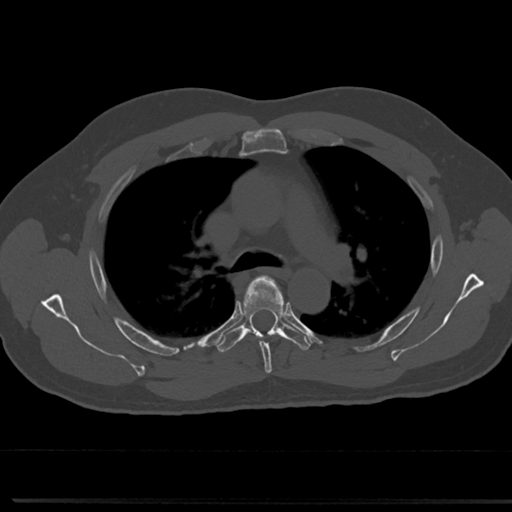
CT including the spine, one axial slice. Reconstruction kernel Br40s/3. Bone window (W 1800 / L 400 HU). 0.5 mm slice thickness. 512 × 512 image matrix, field of view 355 × 355 mm. Patient: male, 61 years. From the clinical record (not read from this slice): primary cancer: prostate.
Annotated regions visible in this slice (semi-automatically segmented with operator editing):
- T4 vertebra: bounding box (x1, y1, x2, y2) in pixels: (241, 275, 288, 364)
- T5 vertebra: (220, 306, 310, 350)